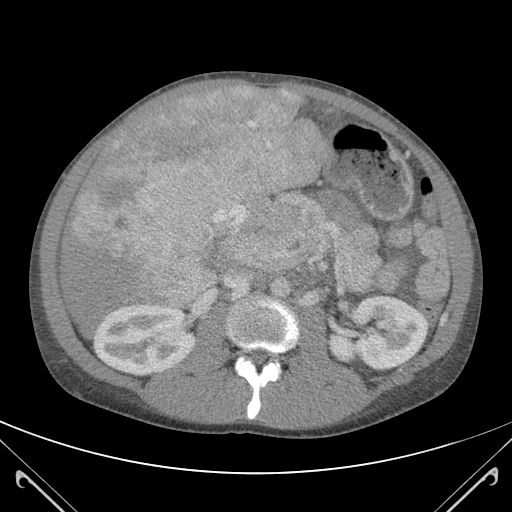
Contrast-enhanced abdominal CT (liver protocol), one axial slice; position 57 of 118 along the scan axis; 120 kVp; soft-tissue window (W 400 / L 40 HU); 3 mm slice thickness; 512 × 512 image matrix, field of view 380 × 380 mm. Case-level facts recorded for this patient, not image findings: diagnosis: hepatocellular carcinoma (patient treated with transarterial chemoembolisation; whether this scan precedes or follows treatment is not stated here); TNM stage (as recorded): Stage-IIIB; Child-Pugh class: A; tumour nodularity: uninodular.
Annotated regions visible in this slice (semi-automatically segmented with operator editing):
- abdominal aorta: bounding box <270,278,290,298> (left, top, right, bottom; pixels)
- liver parenchyma outside the tumour (the mass and vessels are separate outlines, so this box may not span the whole liver): <59,86,327,331>
- mass: <71,88,323,310>
- liver vessels: <191,99,306,306>